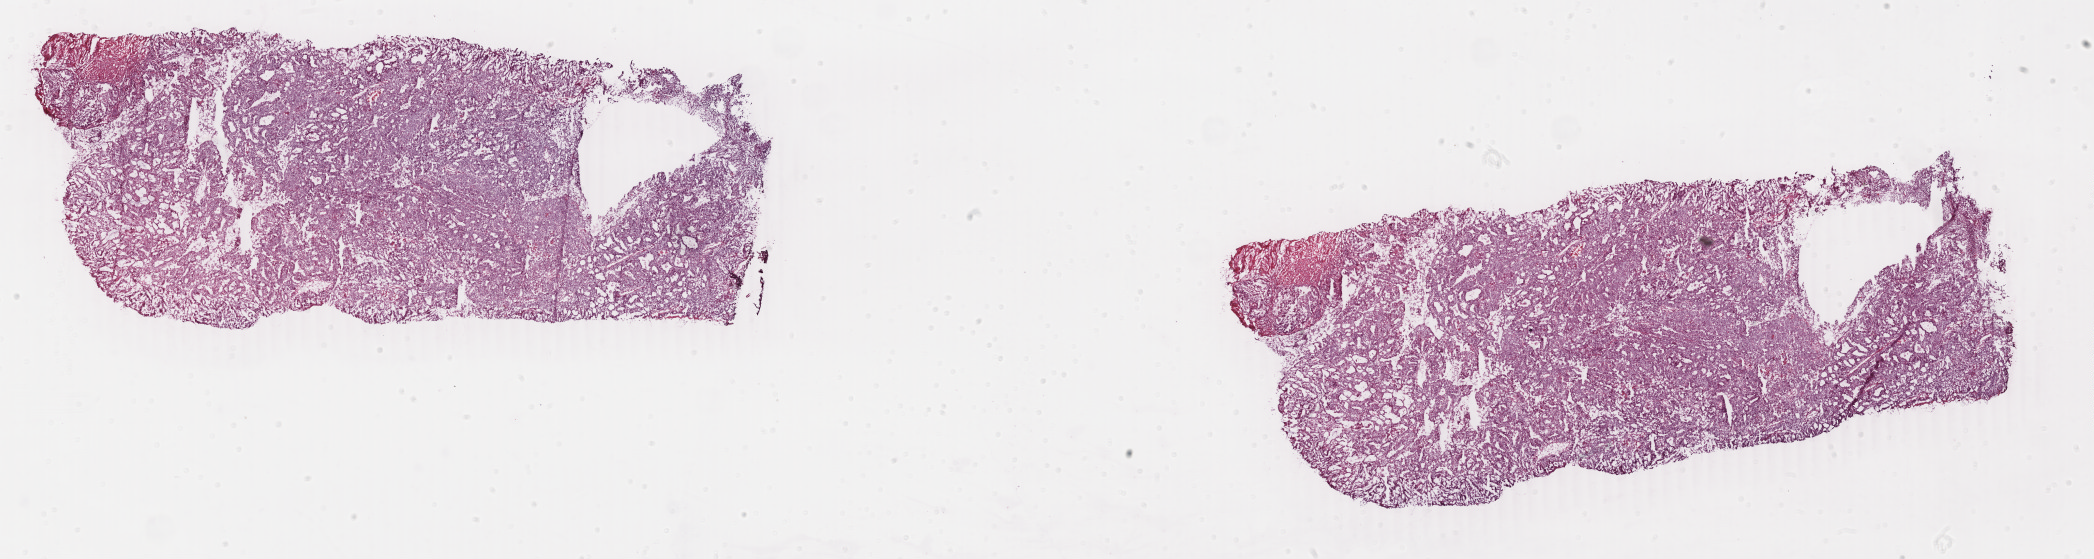
Whole-slide histology image, H&E, a low-resolution overview of the entire scanned area, about 33.3 x 8.9 mm (acquisition: 40x scan); frozen section from the bottom of the tissue portion; uterus, primary tumour sample. Female patient; age at initial diagnosis 60 years. Histologic grade: G1 (well differentiated). Composition of this section per pathologist review: tumour cells 85%, tumour nuclei 90%, normal cells 6%, stromal cells 4%, necrosis 5%. Inflammatory infiltration, as recorded: lymphocyte infiltration 3%, monocyte infiltration 0%, neutrophil infiltration 2%.
* FIGO stage: IIB
* pathologic diagnosis: Endometrioid adenocarcinoma, NOS